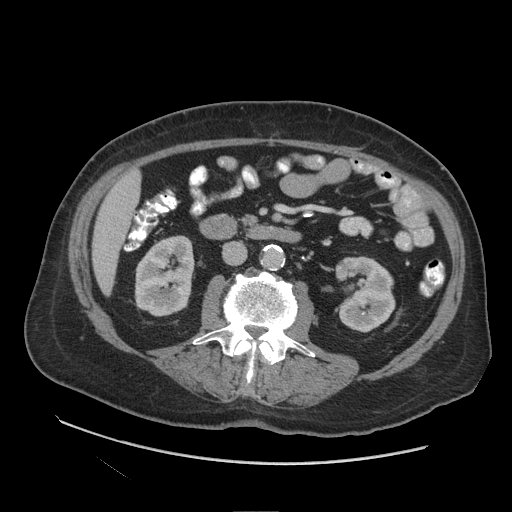
Contrast-enhanced abdominal CT (liver protocol), one axial slice. Position 28 of 109 along the scan axis. Reconstruction kernel STANDARD. 140 kVp. Soft-tissue window (W 400 / L 40 HU). 512 × 512 image matrix, field of view 420 × 420 mm. From the clinical record (not read from this slice): diagnosis: hepatocellular carcinoma (patient treated with transarterial chemoembolisation; whether this scan precedes or follows treatment is not stated here); TNM stage (as recorded): Stage-I; Child-Pugh class: A.
Annotated regions visible in this slice (semi-automatically segmented with operator editing):
- liver parenchyma outside the tumour (the mass and vessels are separate outlines, so this box may not span the whole liver): bounding box (x1, y1, x2, y2) in pixels: (92, 170, 140, 295)